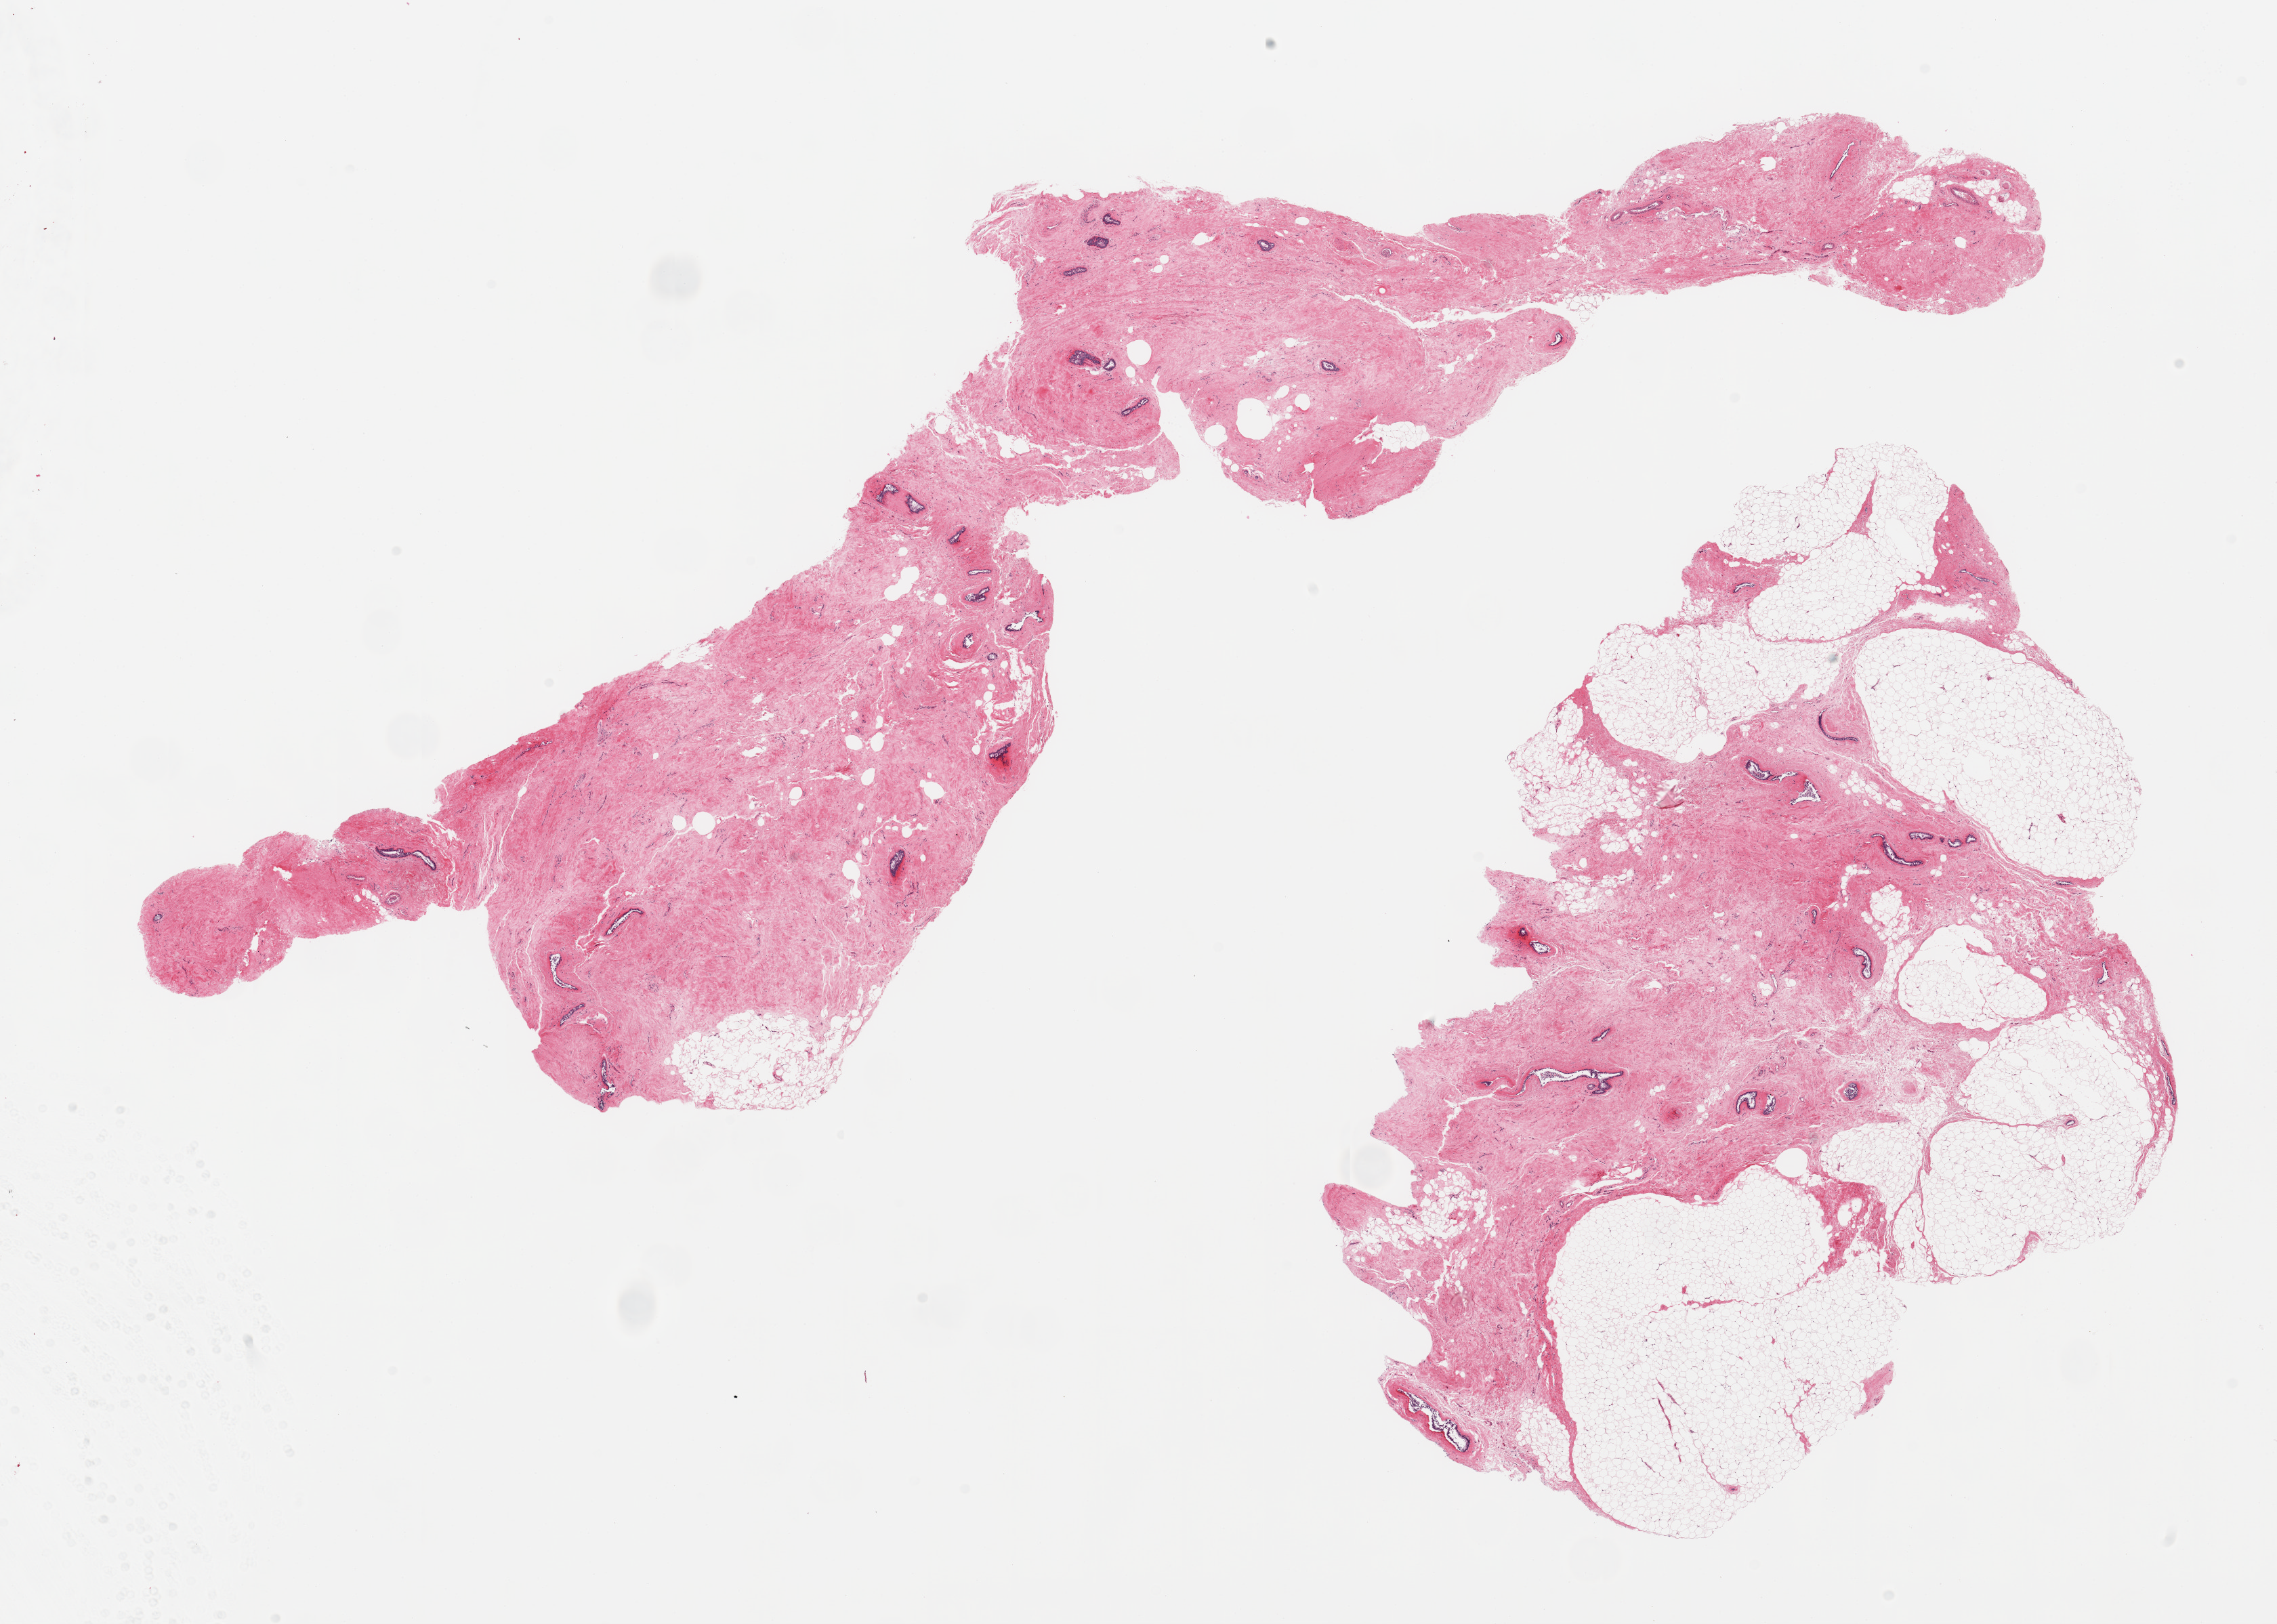
Digitized hematoxylin and eosin (H&E)-stained section, brightfield — a low-resolution overview of the entire scanned area, about 26.6 x 19.0 mm. PAXgene-fixed, paraffin-embedded tissue. Section of breast (target tissue). Donor tissue sample. Donor sex: male.
- pathologist's review note for this sample: 2 pieces; fibrosis and ducts gynecomastoid hyperplasia